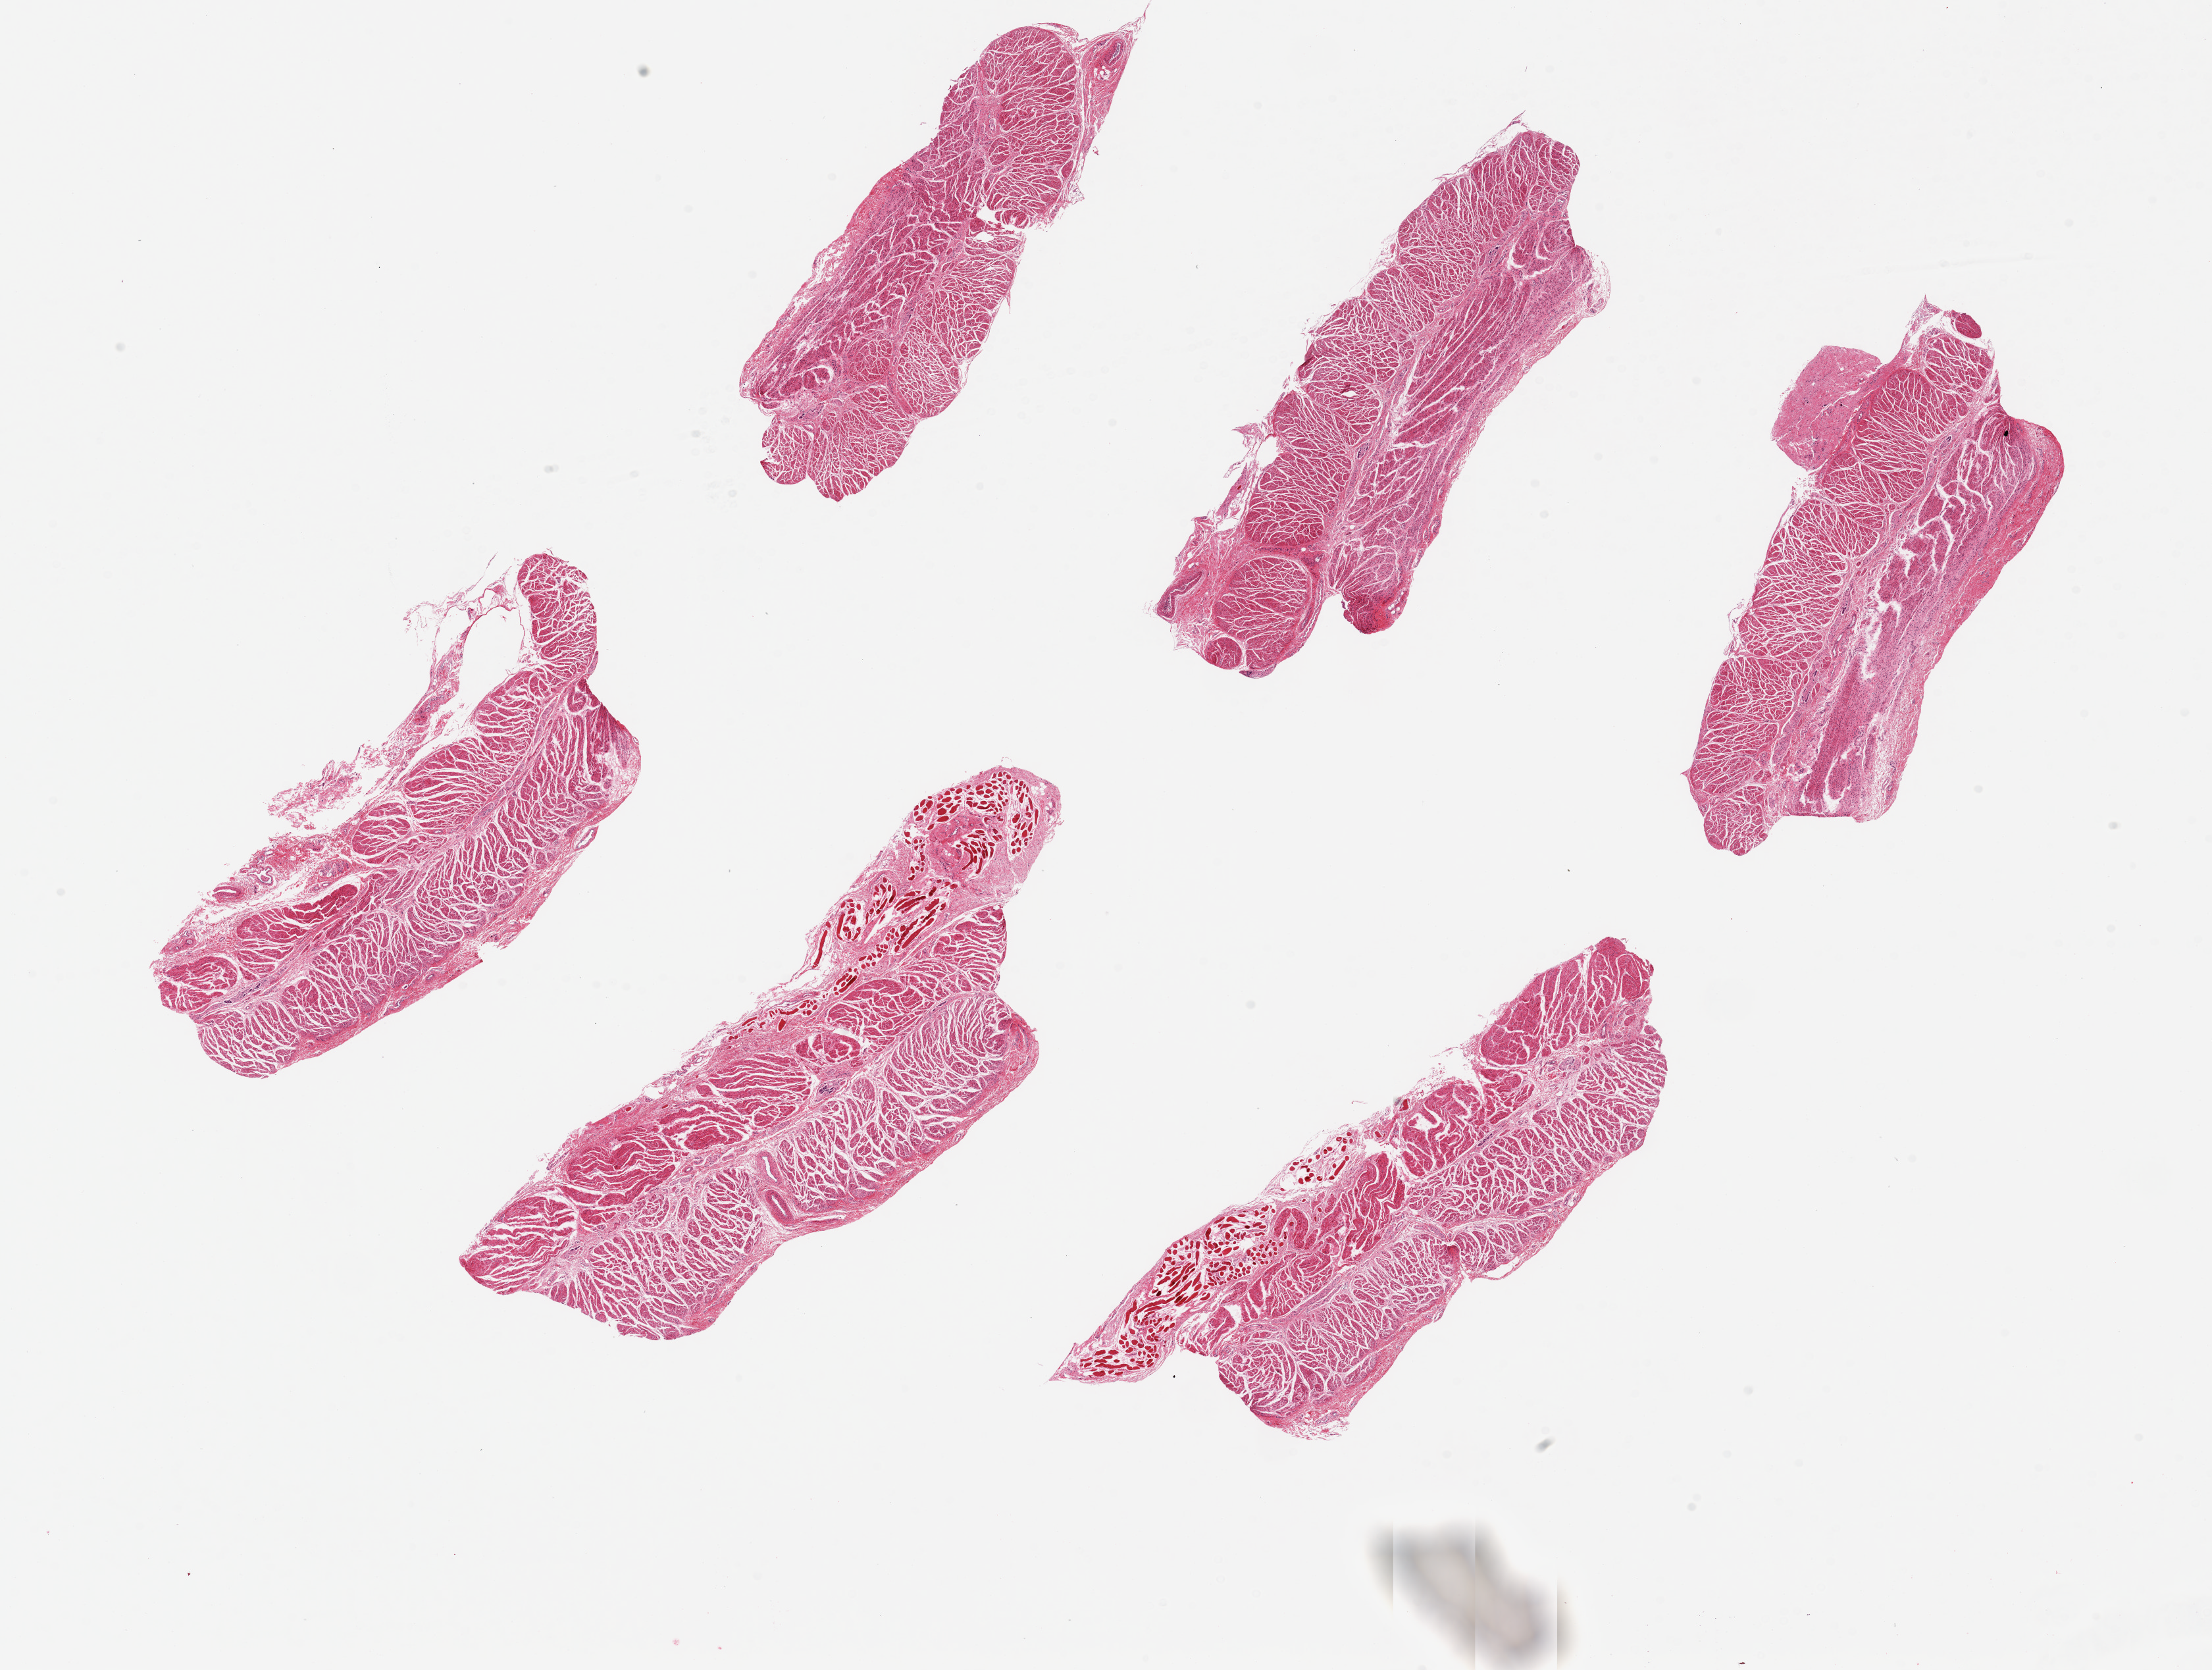
Digitized hematoxylin and eosin (H&E)-stained section, brightfield — a low-resolution overview of the entire scanned area, about 26.6 x 20.1 mm; PAXgene-fixed, paraffin-embedded tissue; sampled site (target tissue): gastroesophageal junction; tissue donor sample. Donor: male.
Pathologist's review note for this sample: 6 pieces ~7x2mm, all muscularis.